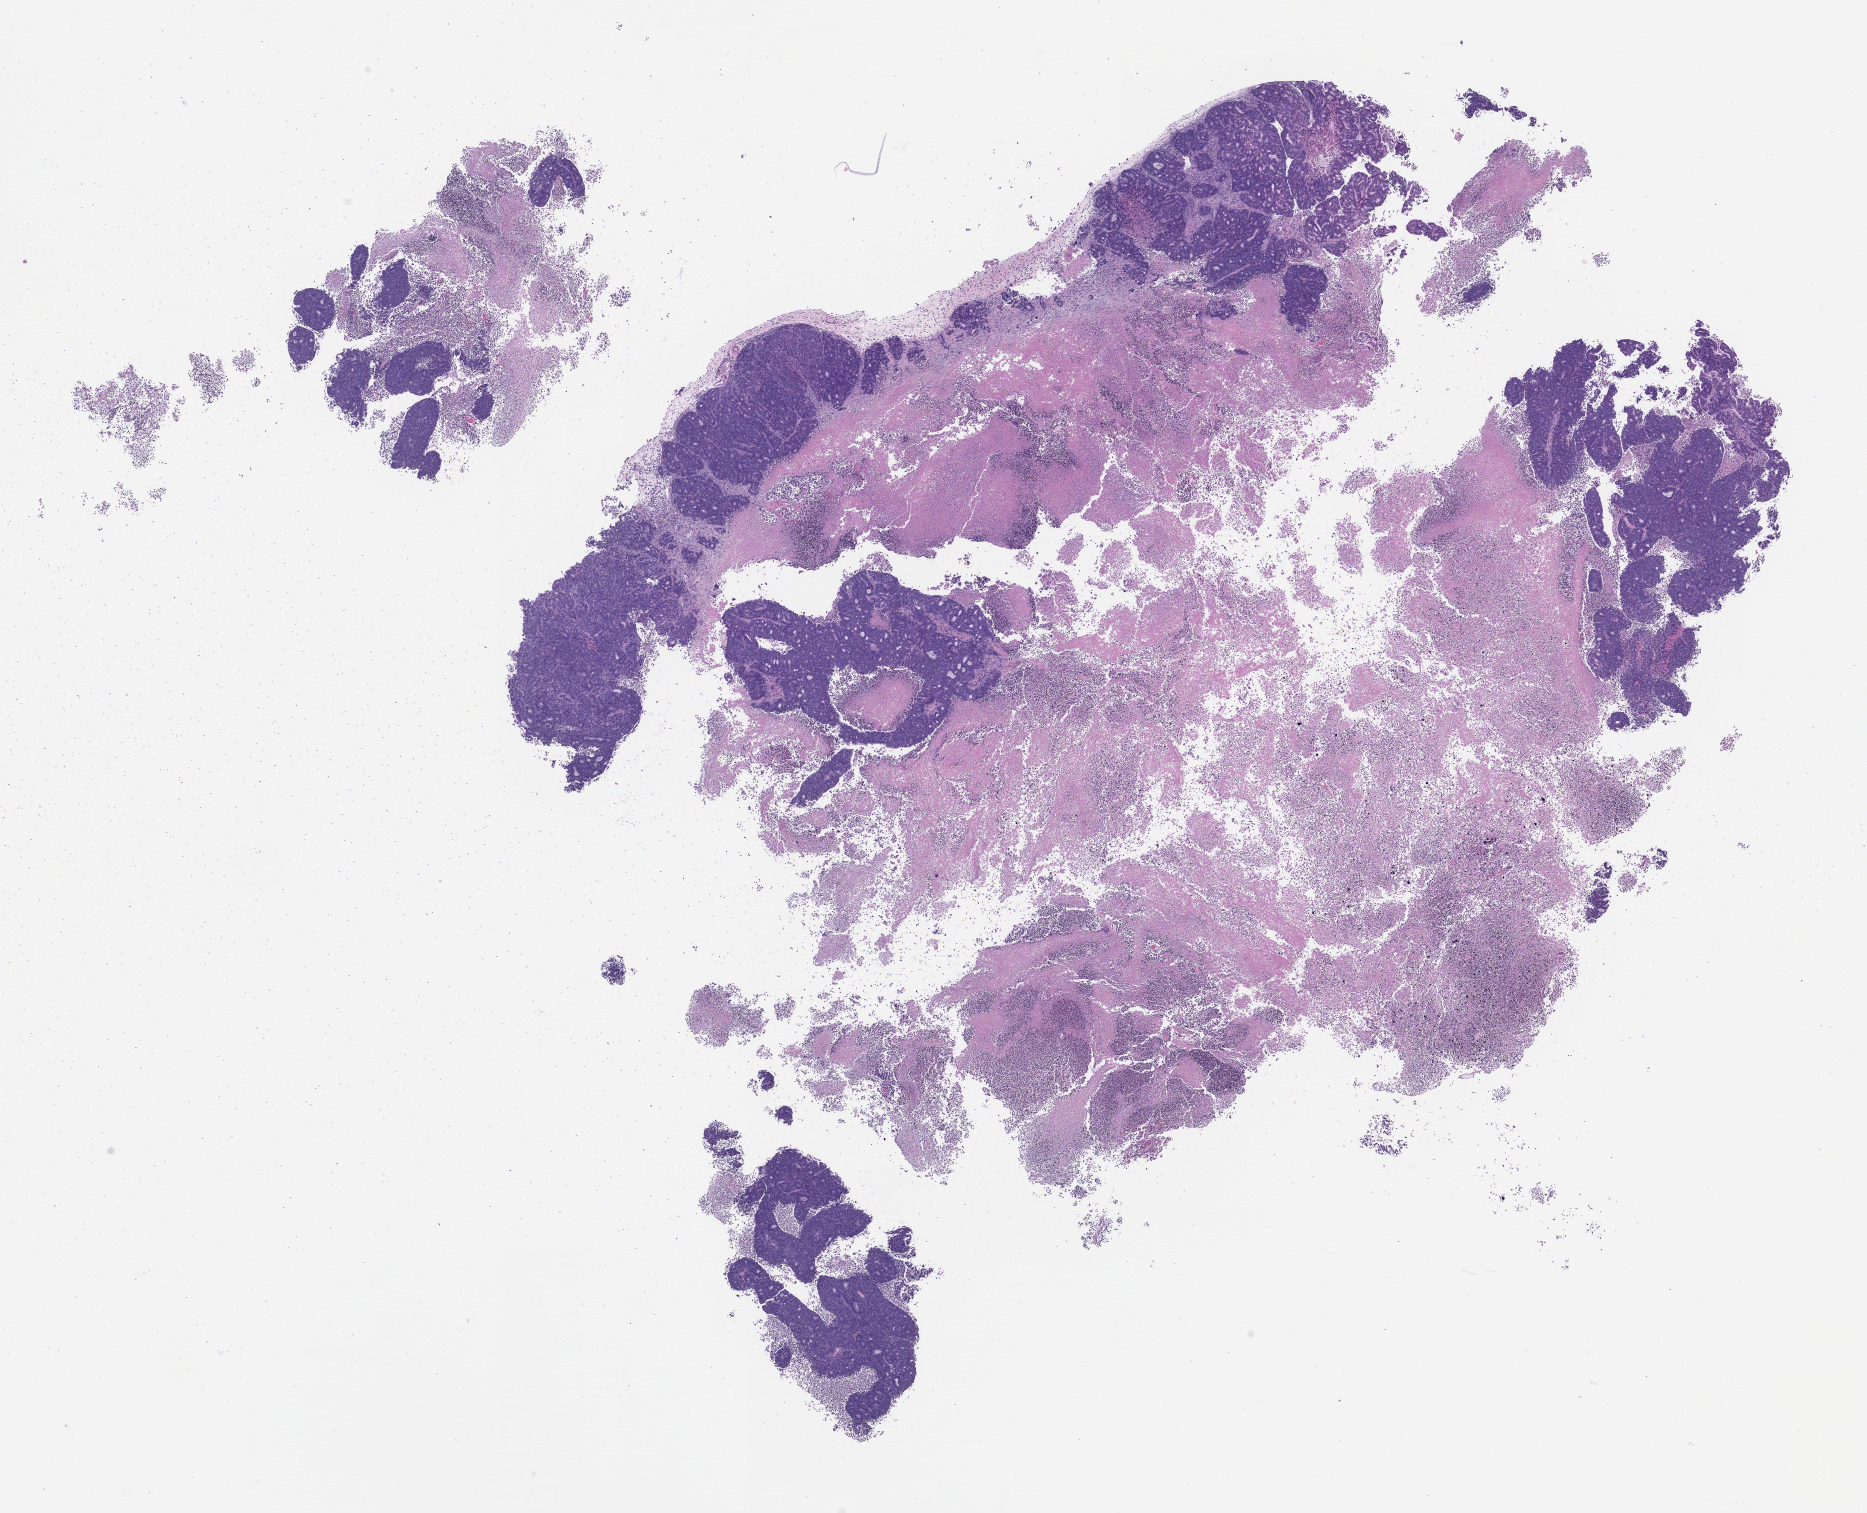
Whole-slide image, hematoxylin and eosin (H&E): patient-derived xenograft (human tumor grown in a mouse), passage 2 — a low-resolution overview of the entire scanned area, about 15.0 x 12.2 mm; FFPE section; originating tumor site category: colon.
Originating patient diagnosis: Colon Adenocarcinoma.